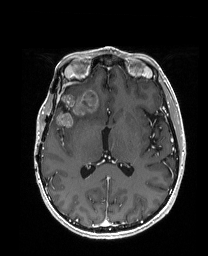
Brain MRI from a brain-tumour surgery series, one axial slice; position 90 of 192 along the scan axis; T1-weighted post-contrast; 208 × 256 image matrix, field of view 203 × 250 mm. Case-level facts recorded for this patient, not image findings: histopathology: Metastatic Carcinoma from Breast primary; tumour location: Right Frontal.
Outlined on this slice (manually delineated by an expert):
- previous resection cavity: bounding box (x1, y1, x2, y2) in pixels: (58, 101, 67, 111)
- tumour: (55, 88, 104, 126)